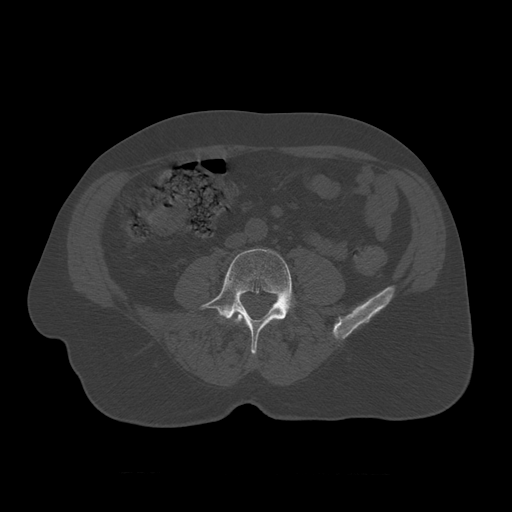
CT including the spine, one axial slice. Slice 278 of 450 in the series (ordered by position). 120 kVp. Bone window (W 1800 / L 400 HU). 512 × 512 image matrix, field of view 405 × 405 mm. Patient age 75 years. Case-level facts recorded for this patient, not image findings: primary cancer: prostate.
Structures marked on this image (semi-automatic segmentation, software-assisted and operator-edited):
- L3 vertebra: bounding box [x1, y1, x2, y2] px = [234, 315, 245, 324]
- L4 vertebra: [199, 248, 296, 356]
- L5 vertebra: [229, 303, 295, 321]